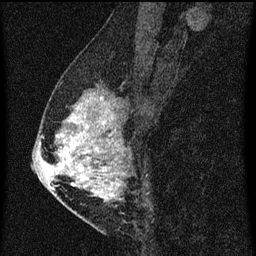
Breast MRI (dynamic contrast-enhanced), one sagittal slice; slice 25 of 60 in the series (ordered by position); dynamic contrast-enhanced series, image 2 of 3 at this slice position (ordered by acquisition); 1.5 T; TE 4.2 ms, TR 8 ms; 256 × 256 image matrix. Patient: female, 47 years.
Structures marked on this image (semi-automatic segmentation, software-assisted and operator-edited):
- analysis volume of interest (the breast-tissue region the enhancement analysis was run in; not a lesion): bounding box <50,80,138,203> (left, top, right, bottom; pixels)
- tumour enhancement mask (voxels above the 70 % enhancement threshold inside the analysis volume of interest): <57,98,127,199>